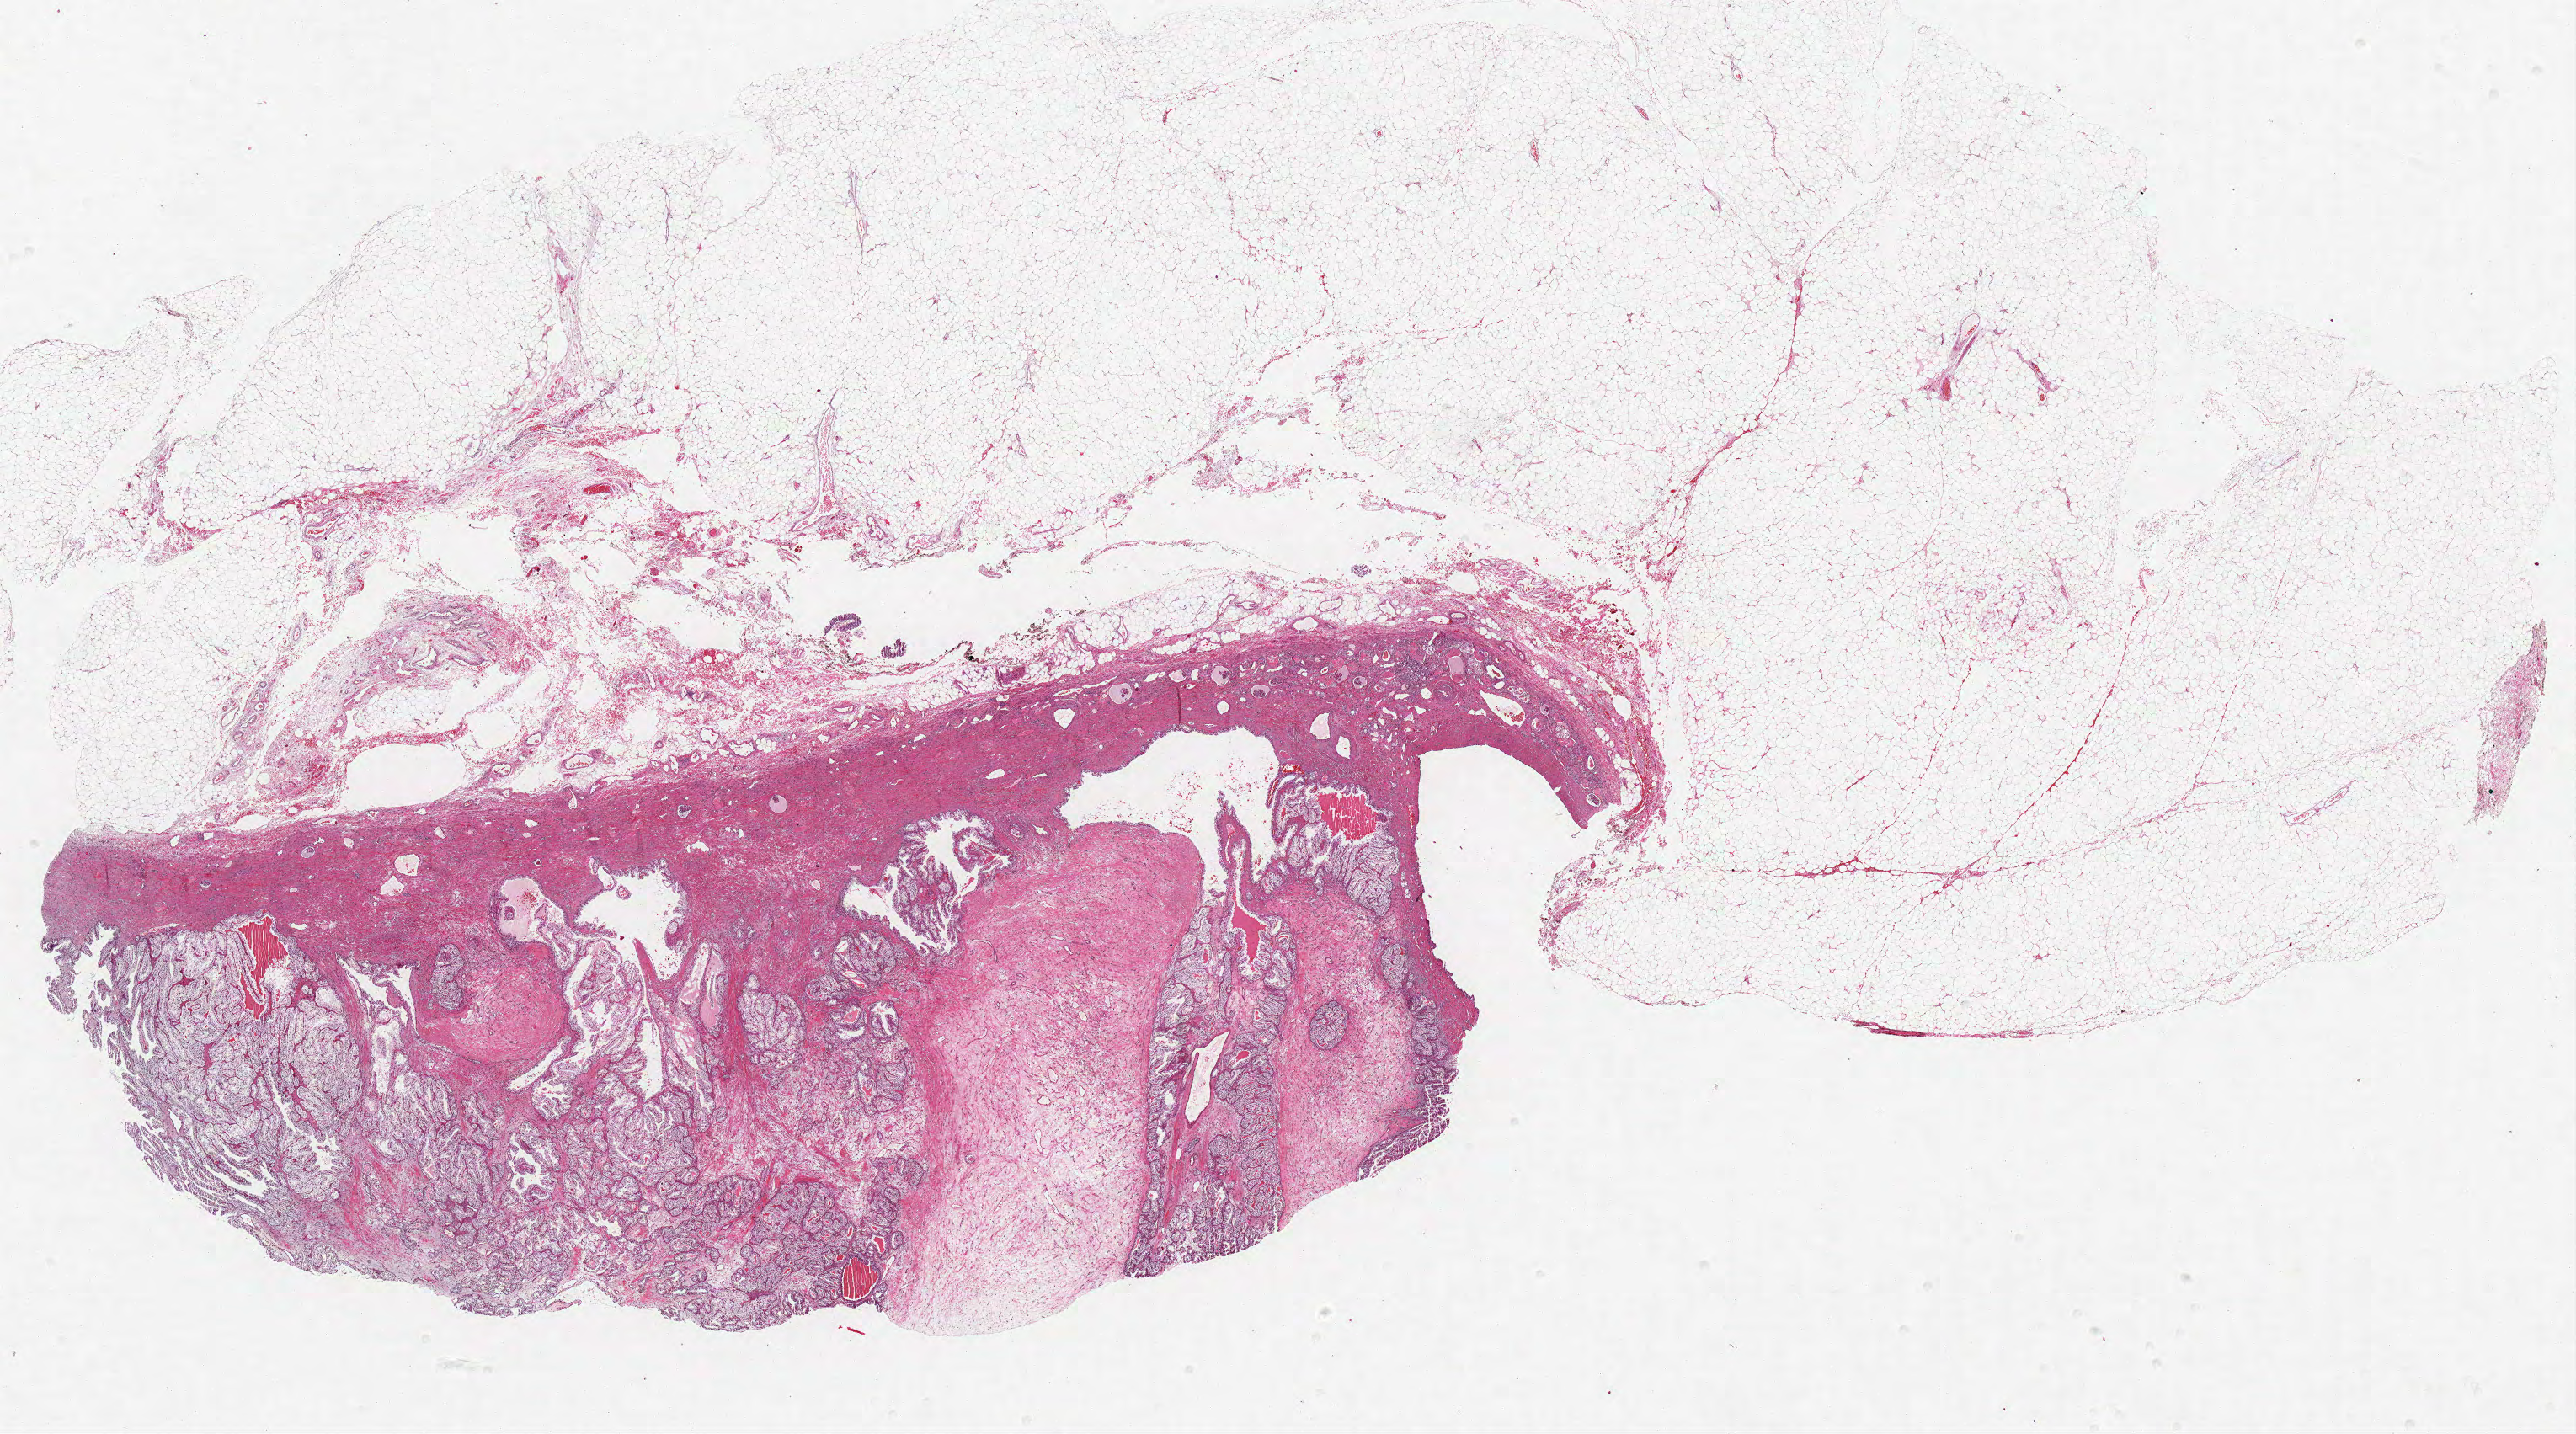
H&E whole-slide image — a low-resolution overview of the entire scanned area, about 24.5 x 13.6 mm (from a 40x scan); formalin-fixed paraffin-embedded (FFPE) diagnostic section; sample: primary tumour, kidney. Patient: female, age at initial diagnosis 74 years. Histologic grade: G2 (moderately differentiated).
Pathologic diagnosis: Clear cell adenocarcinoma, NOS. Lymph nodes positive (case pathology): 0 of 2 examined. AJCC pathologic stage: I.